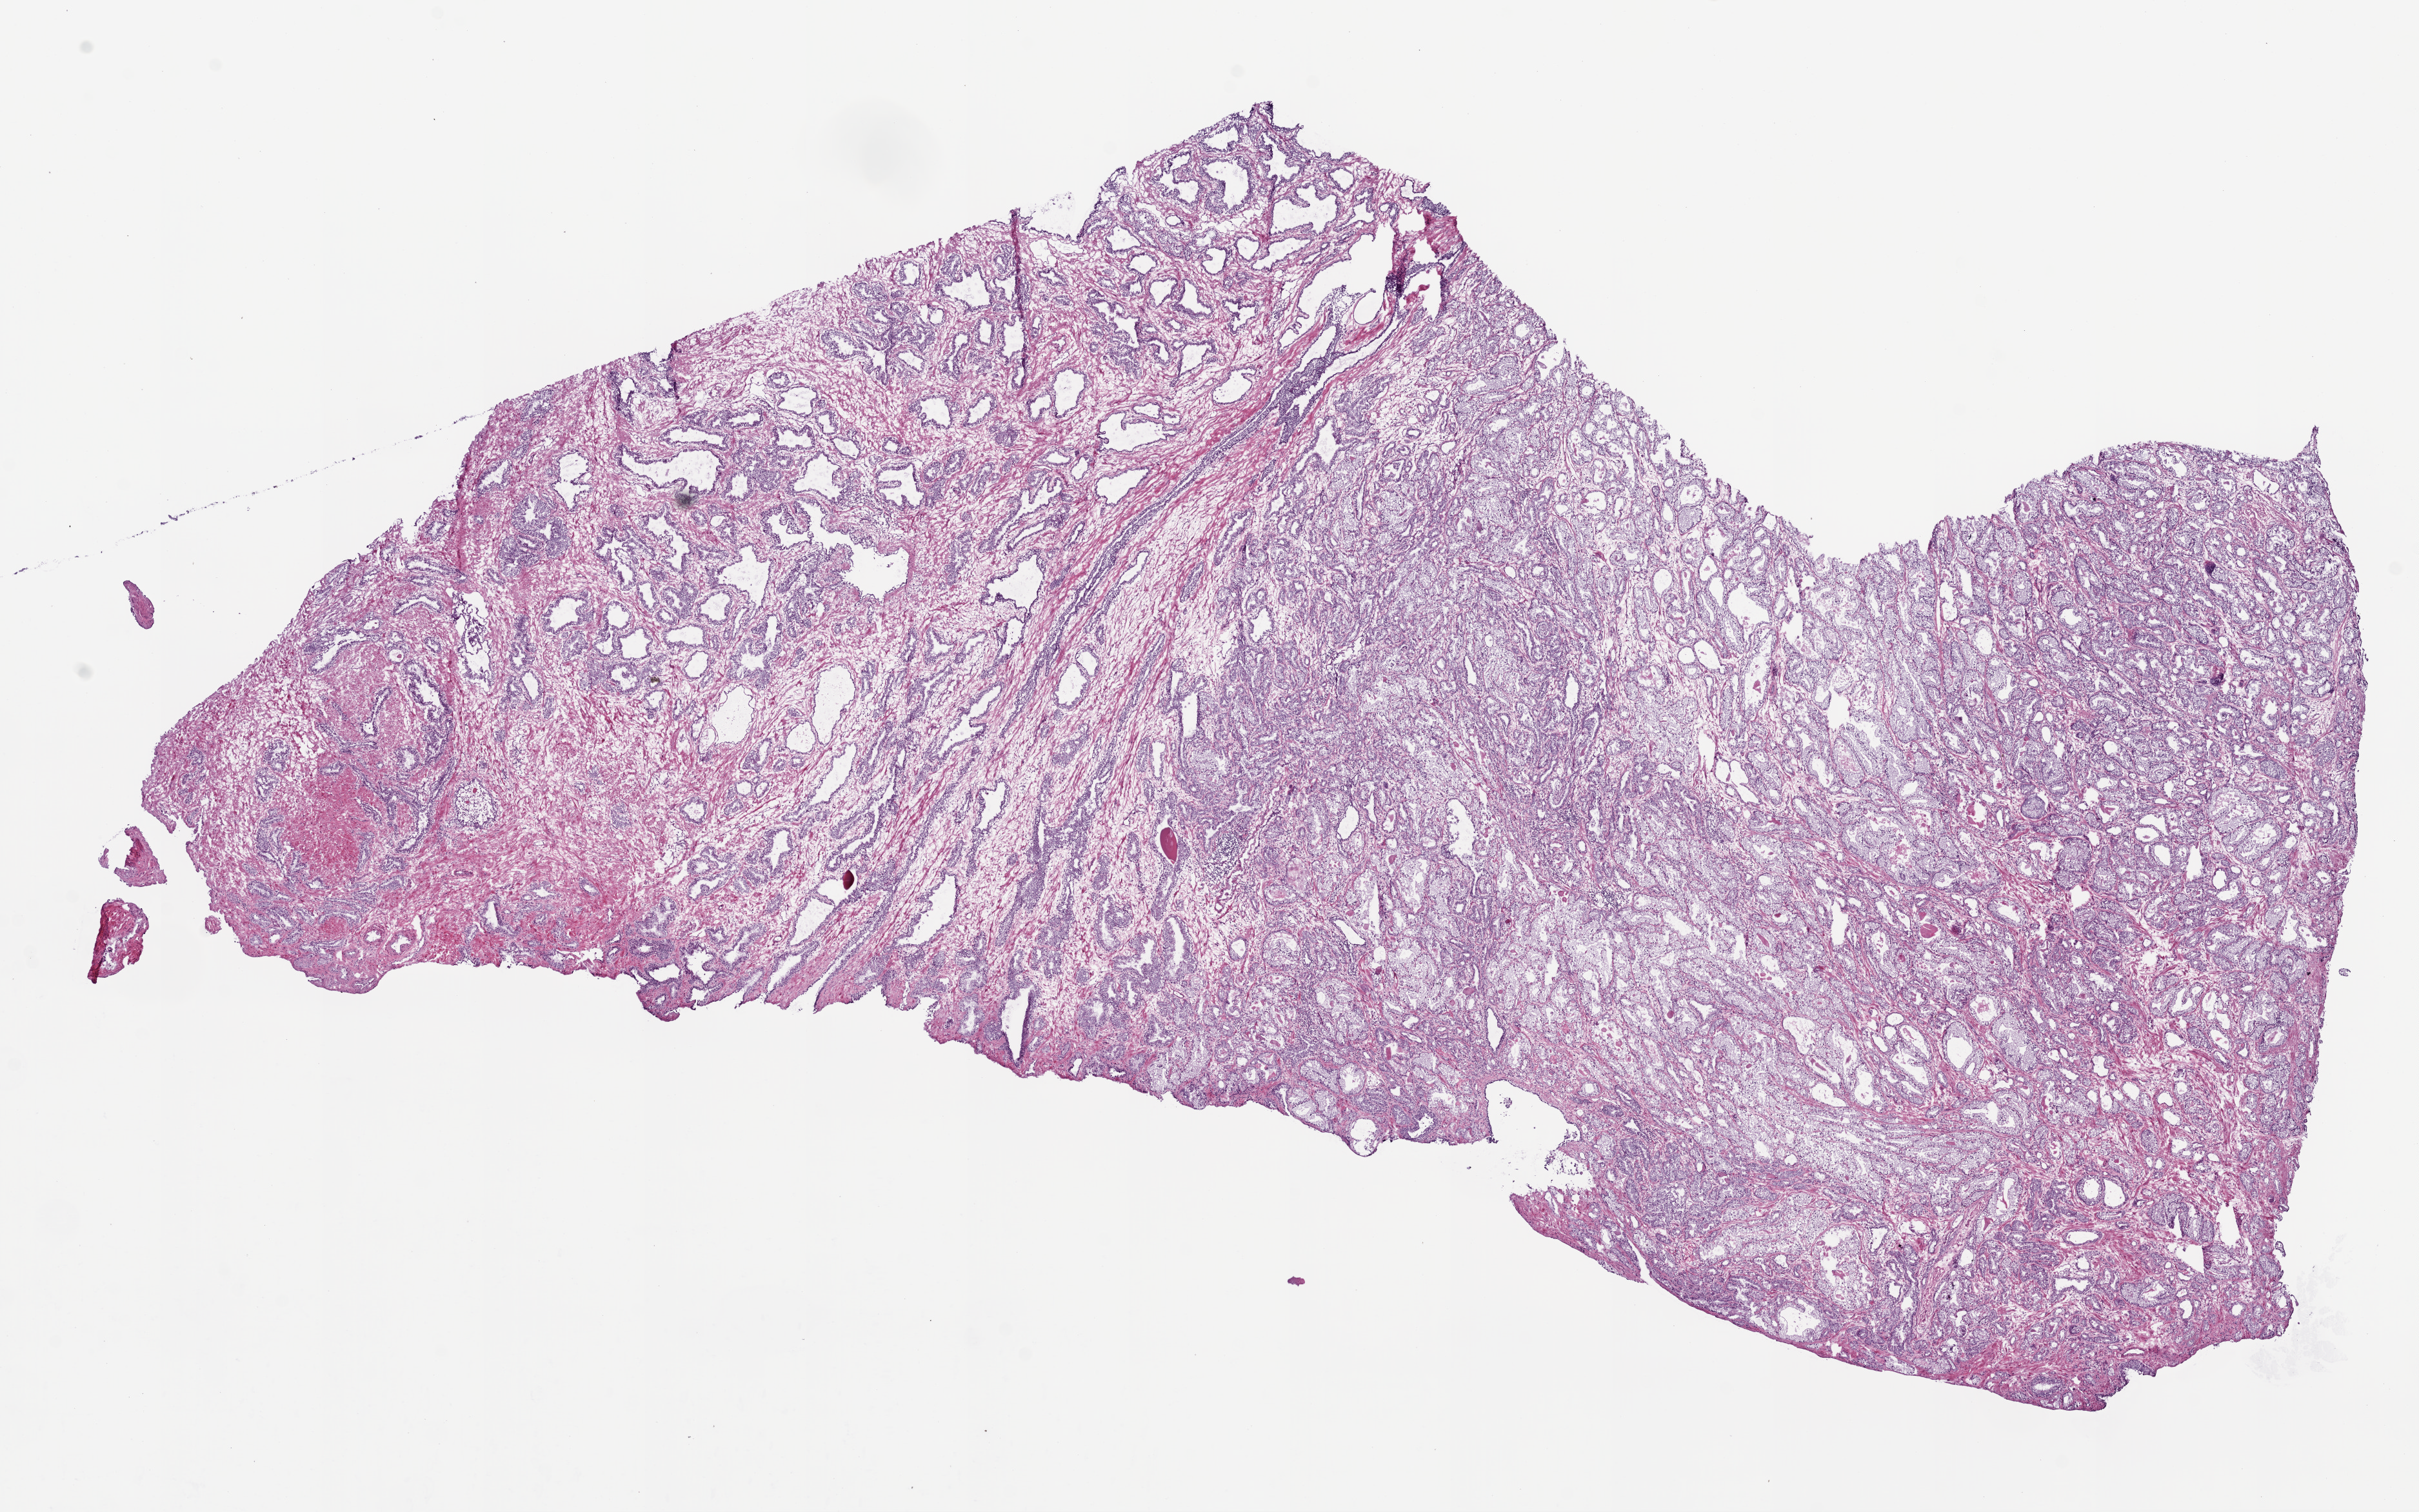
Whole-slide histology image, H&E-stained, a low-resolution overview of the entire scanned area, about 15.0 x 9.4 mm (acquisition: 20x scan), frozen section, prostate, primary tumour sample. Male patient; age at initial diagnosis 47 years. Gleason score: 7 (3+4). Pathologist review of this section (percent, as recorded): tumour cells 60%, tumour nuclei 70%, normal cells 25%, stromal cells 15%, necrosis 0%. Inflammatory infiltration, as recorded: lymphocyte infiltration 1%, monocyte infiltration 0%, neutrophil infiltration 0%.
* pathologic diagnosis: Acinar cell carcinoma
* lymph nodes positive (case pathology): 0 of 10 examined
* laterality: bilateral